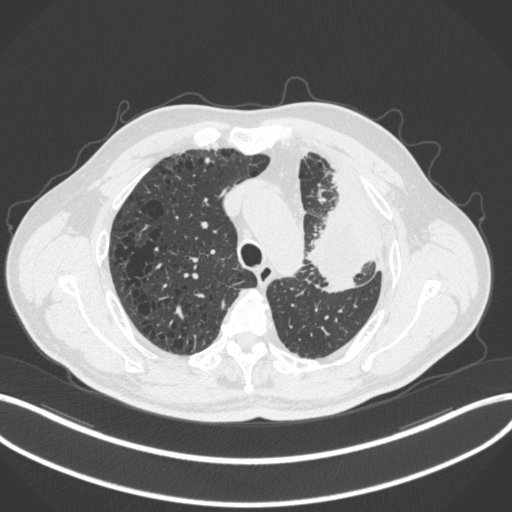
Chest CT, one axial slice. Position 227 of 286 along the scan axis. Lung window (W 1500 / L -600 HU). 512 × 512 image matrix, field of view 400 × 400 mm. Patient: male, 68 years. From the clinical record (not read from this slice): clinical TNM (as recorded): T3 N3 M1.
Structures marked on this image (rectangle marked by the reading radiologist):
- lung tumour (recorded histology: adenocarcinoma): bounding box [x1, y1, x2, y2] px = [308, 196, 375, 294]